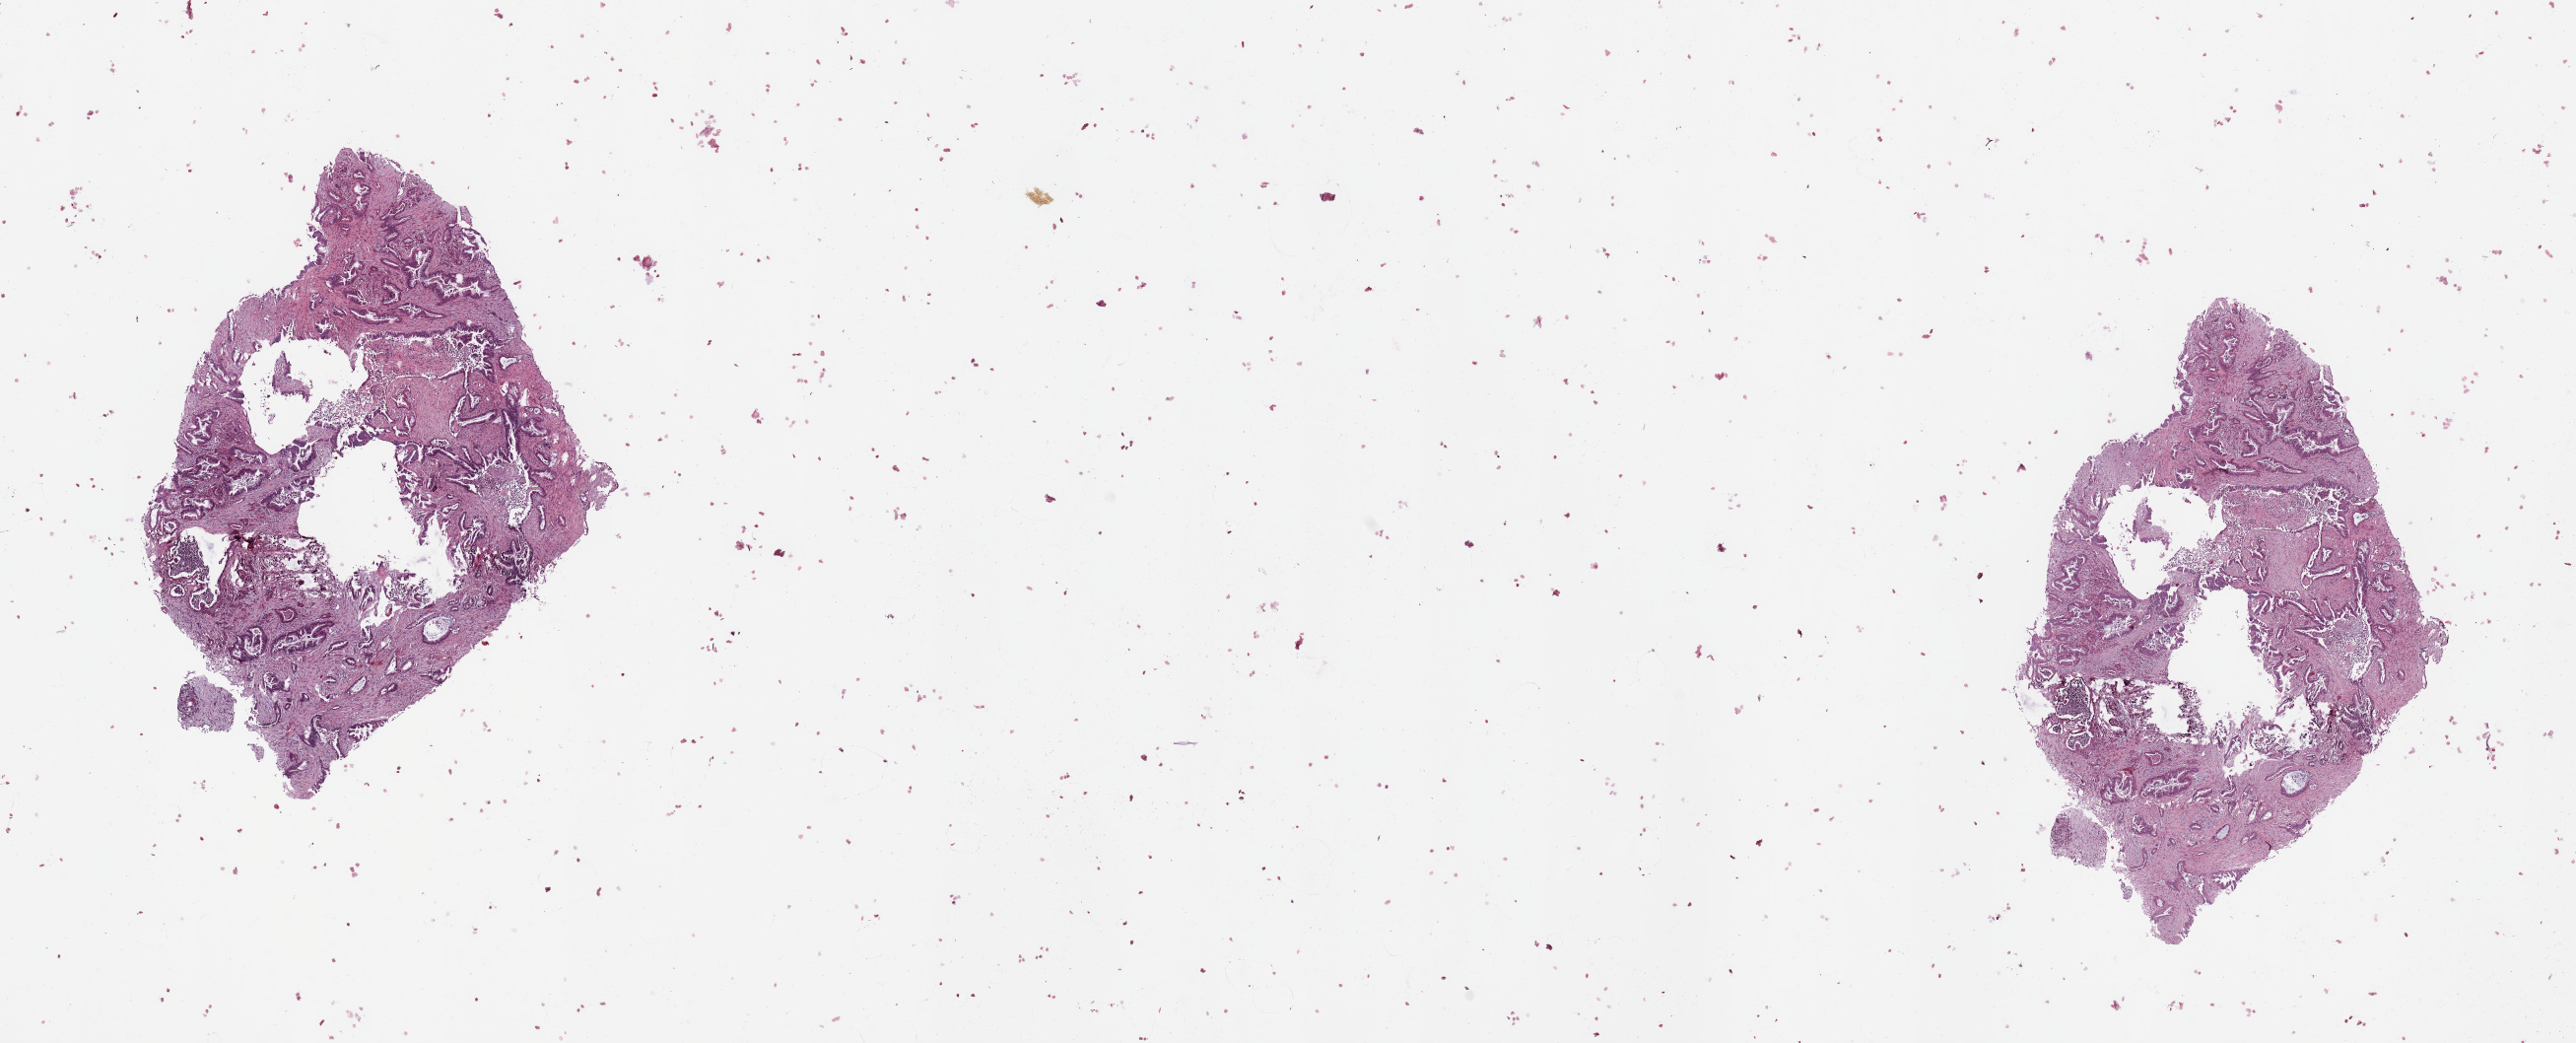
Digitized Hematoxylin and eosin (H&E) stained tissue section (whole slide), shown as a low-resolution overview of the whole scanned area (about 20.7 x 8.4 mm, acquisition: 20x scan). Tumour tissue sample, sampled site: pancreas. Female, 60 y/o. Pathologist review of this section (percent, as recorded): tumour nuclei 40%, necrosis 2%.
Diagnosis: Infiltrating duct carcinoma, NOS.